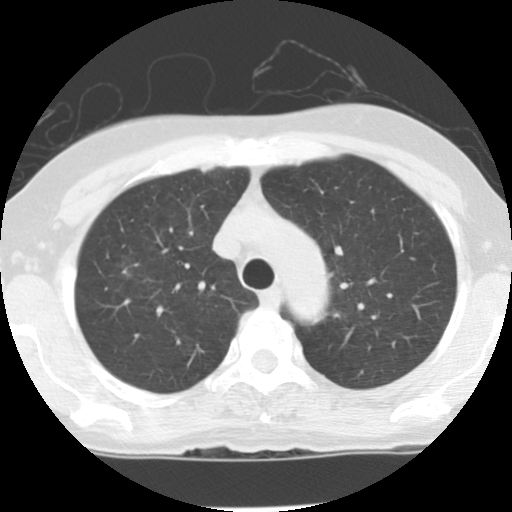
Chest CT (low-dose screening protocol), one axial image. Baseline annual screen. Lung window (W 1500 / L -600 HU). 2.5 mm slice thickness. 512 × 512 image matrix. Female, age 62 years at enrolment.
Expert reader's lesion annotation, bounding box (x1, y1, x2, y2) in pixels: (102, 251, 146, 293). The exam's reader record, not a measurement of the box and not confirmed to be the same lesion: non-calcified nodule or mass ≥4 mm, right upper lobe, 7 × 5 mm, poorly defined margins, ground glass attenuation. Participant outcome: lung cancer diagnosed 875 days after this screen (after the third annual screen) — bronchiolo-alveolar adenocarcinoma, NOS, right upper lobe, stage IA (AJCC 6th edition), 10 mm at pathology.